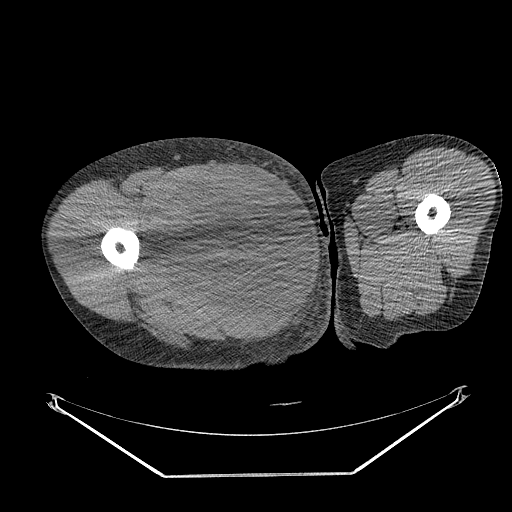
CT of an extremity soft-tissue mass (from a PET/CT study), one axial slice; slice 263 of 311 in the series (ordered by position); reconstruction kernel STANDARD; soft-tissue window (W 400 / L 40 HU); 512 × 512 image matrix. Male patient. From the clinical record (not read from this slice): histological type: undifferentiated - pleiomorphic; grade: high; site of the primary tumour: right thigh.
Outlined on this slice (expert contour drawn on MRI and transferred to this co-registered scan by the dataset authors):
- gross tumour volume including surrounding oedema: bounding box <149,167,268,280> (left, top, right, bottom; pixels)
- gross tumour volume (mass): <157,167,268,279>